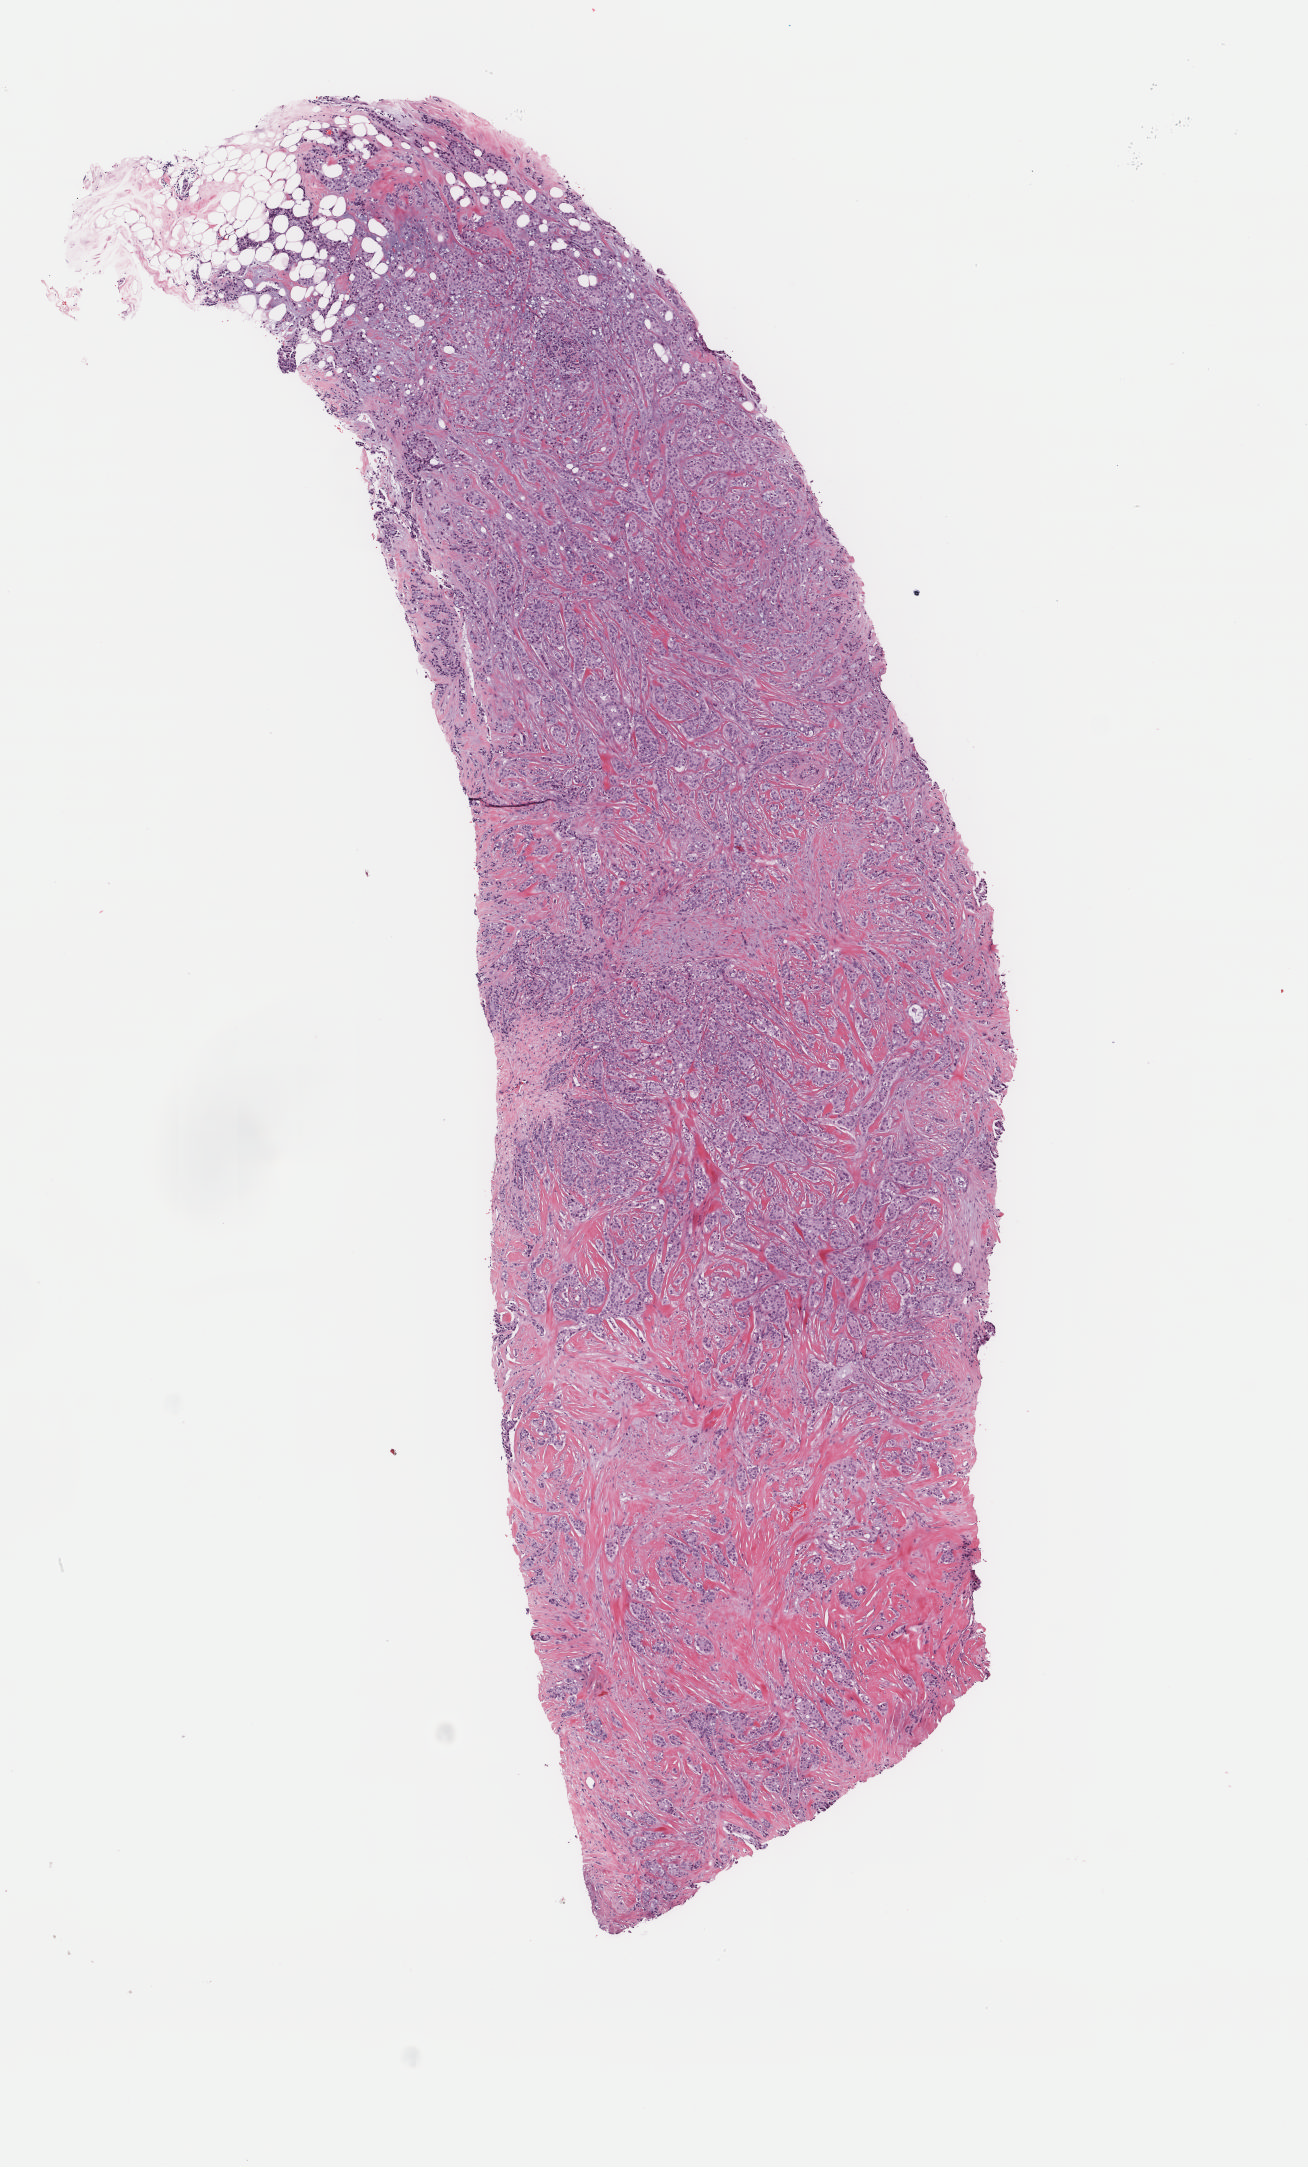
Hematoxylin and eosin (H&E) stained whole-slide image, a low-resolution overview of the entire scanned area, about 5.2 x 8.6 mm (slide scanned at 40x), frozen section from the bottom of the tissue portion, sample: primary tumour, breast. Patient: female, age at initial diagnosis 56 years. Slide review estimates, as recorded: tumour cells 80%, tumour nuclei 80%, normal cells 0%, stromal cells 20%, necrosis 0%. Inflammatory infiltration, as recorded: lymphocyte infiltration 1%, monocyte infiltration 0%, neutrophil infiltration 0%.
AJCC pathologic stage: IIA. Diagnosis: Infiltrating duct carcinoma, NOS. Lymph nodes positive (case pathology): 0 of 4 examined.